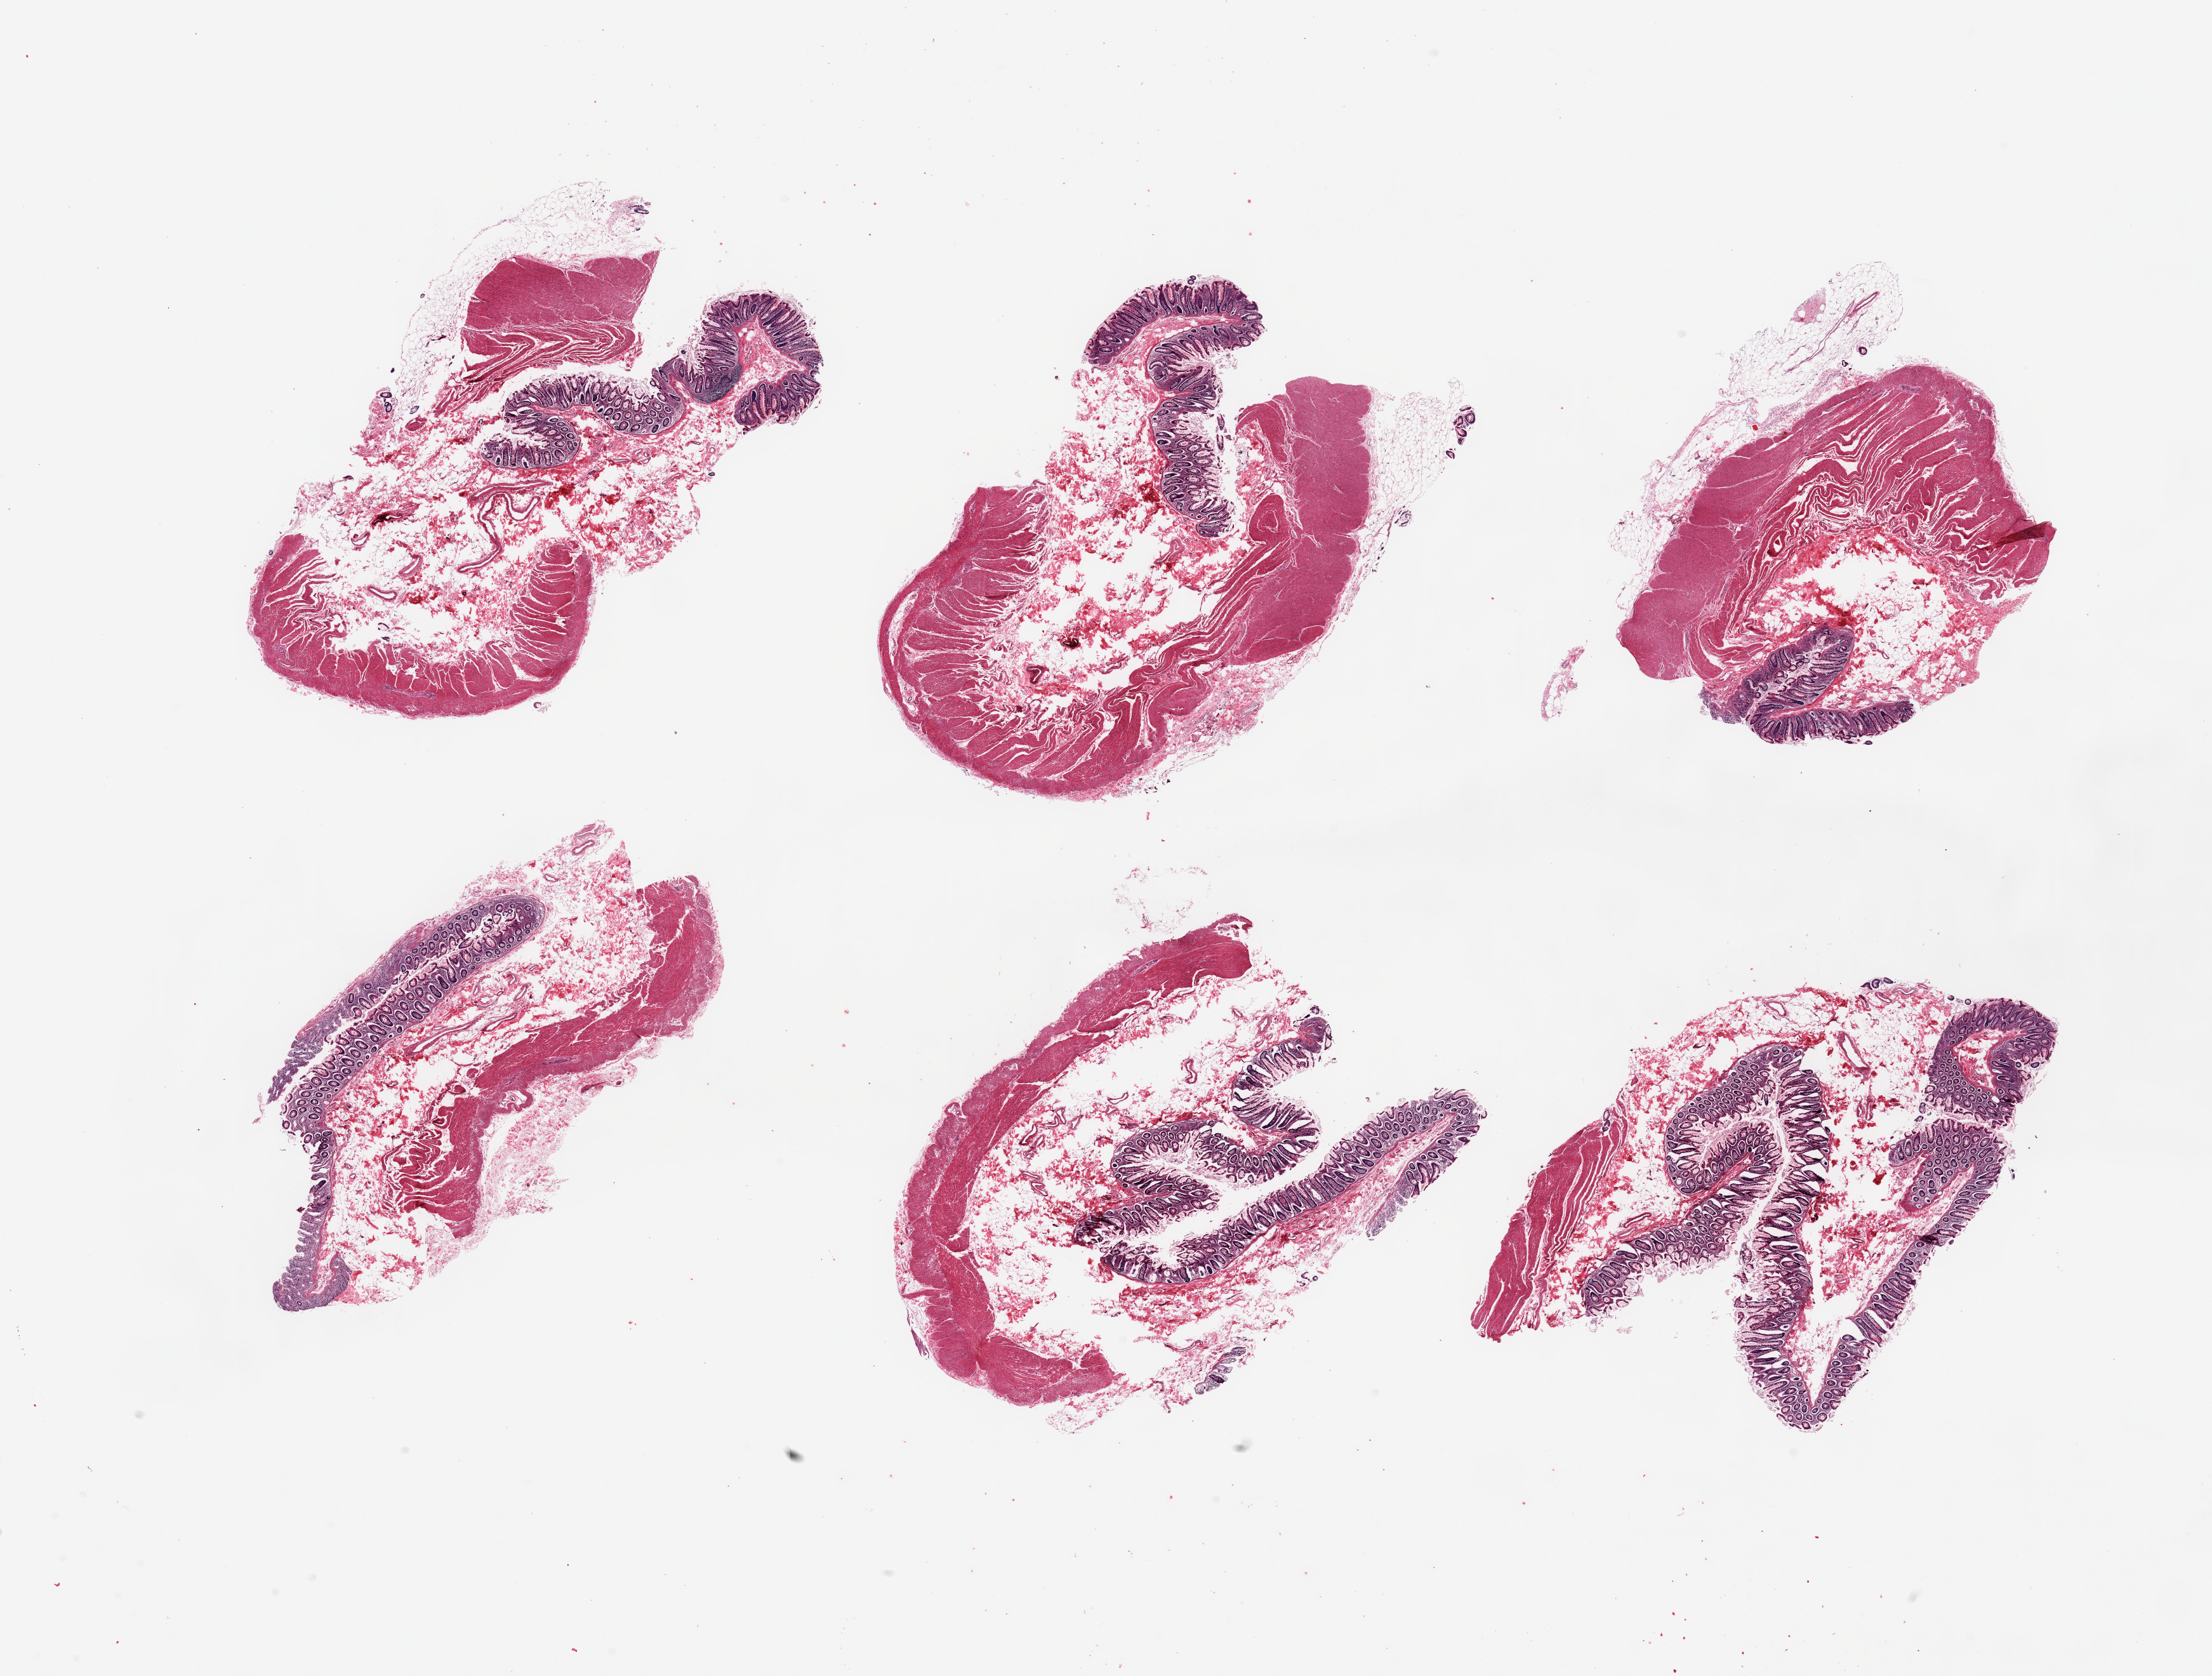
Hematoxylin and eosin (H&E) whole-slide image, a low-resolution overview of the entire scanned area, about 27.6 x 20.9 mm. PAXgene-fixed paraffin-embedded (PFPE) section. Sampled site (target tissue): ileum. Donor tissue sample. Donor: male.
Review note (as recorded): 6 pieces; mucosa and muscularis of colon.